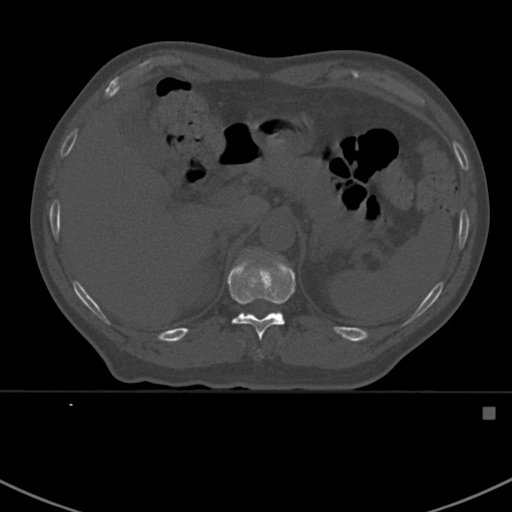
CT including the spine, one axial slice; slice 346 of 412 in the series (ordered by position); 120 kVp; bone window (W 1800 / L 400 HU); 1.5 mm slice thickness; 512 × 512 image matrix, field of view 358 × 358 mm. Patient: male, 59 years. Case-level facts recorded for this patient, not image findings: primary cancer: prostate.
Structures marked on this image (semi-automatically segmented with operator editing):
- T11 vertebra: bounding box (x1, y1, x2, y2) in pixels: (227, 251, 295, 357)